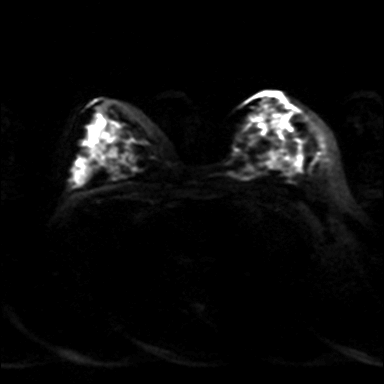
Breast MRI, one axial slice; slice 23 of 36 in the series (ordered by position); diffusion-weighted series; image 2 of 4 stored at this slice position (different b-values; order by instance number); 3 T; 384 × 384 image matrix, field of view 320 × 320 mm. Female patient.
Annotated regions visible in this slice (manually delineated by an expert):
- tumour on diffusion-weighted imaging: bounding box (x1, y1, x2, y2) in pixels: (276, 118, 287, 127)